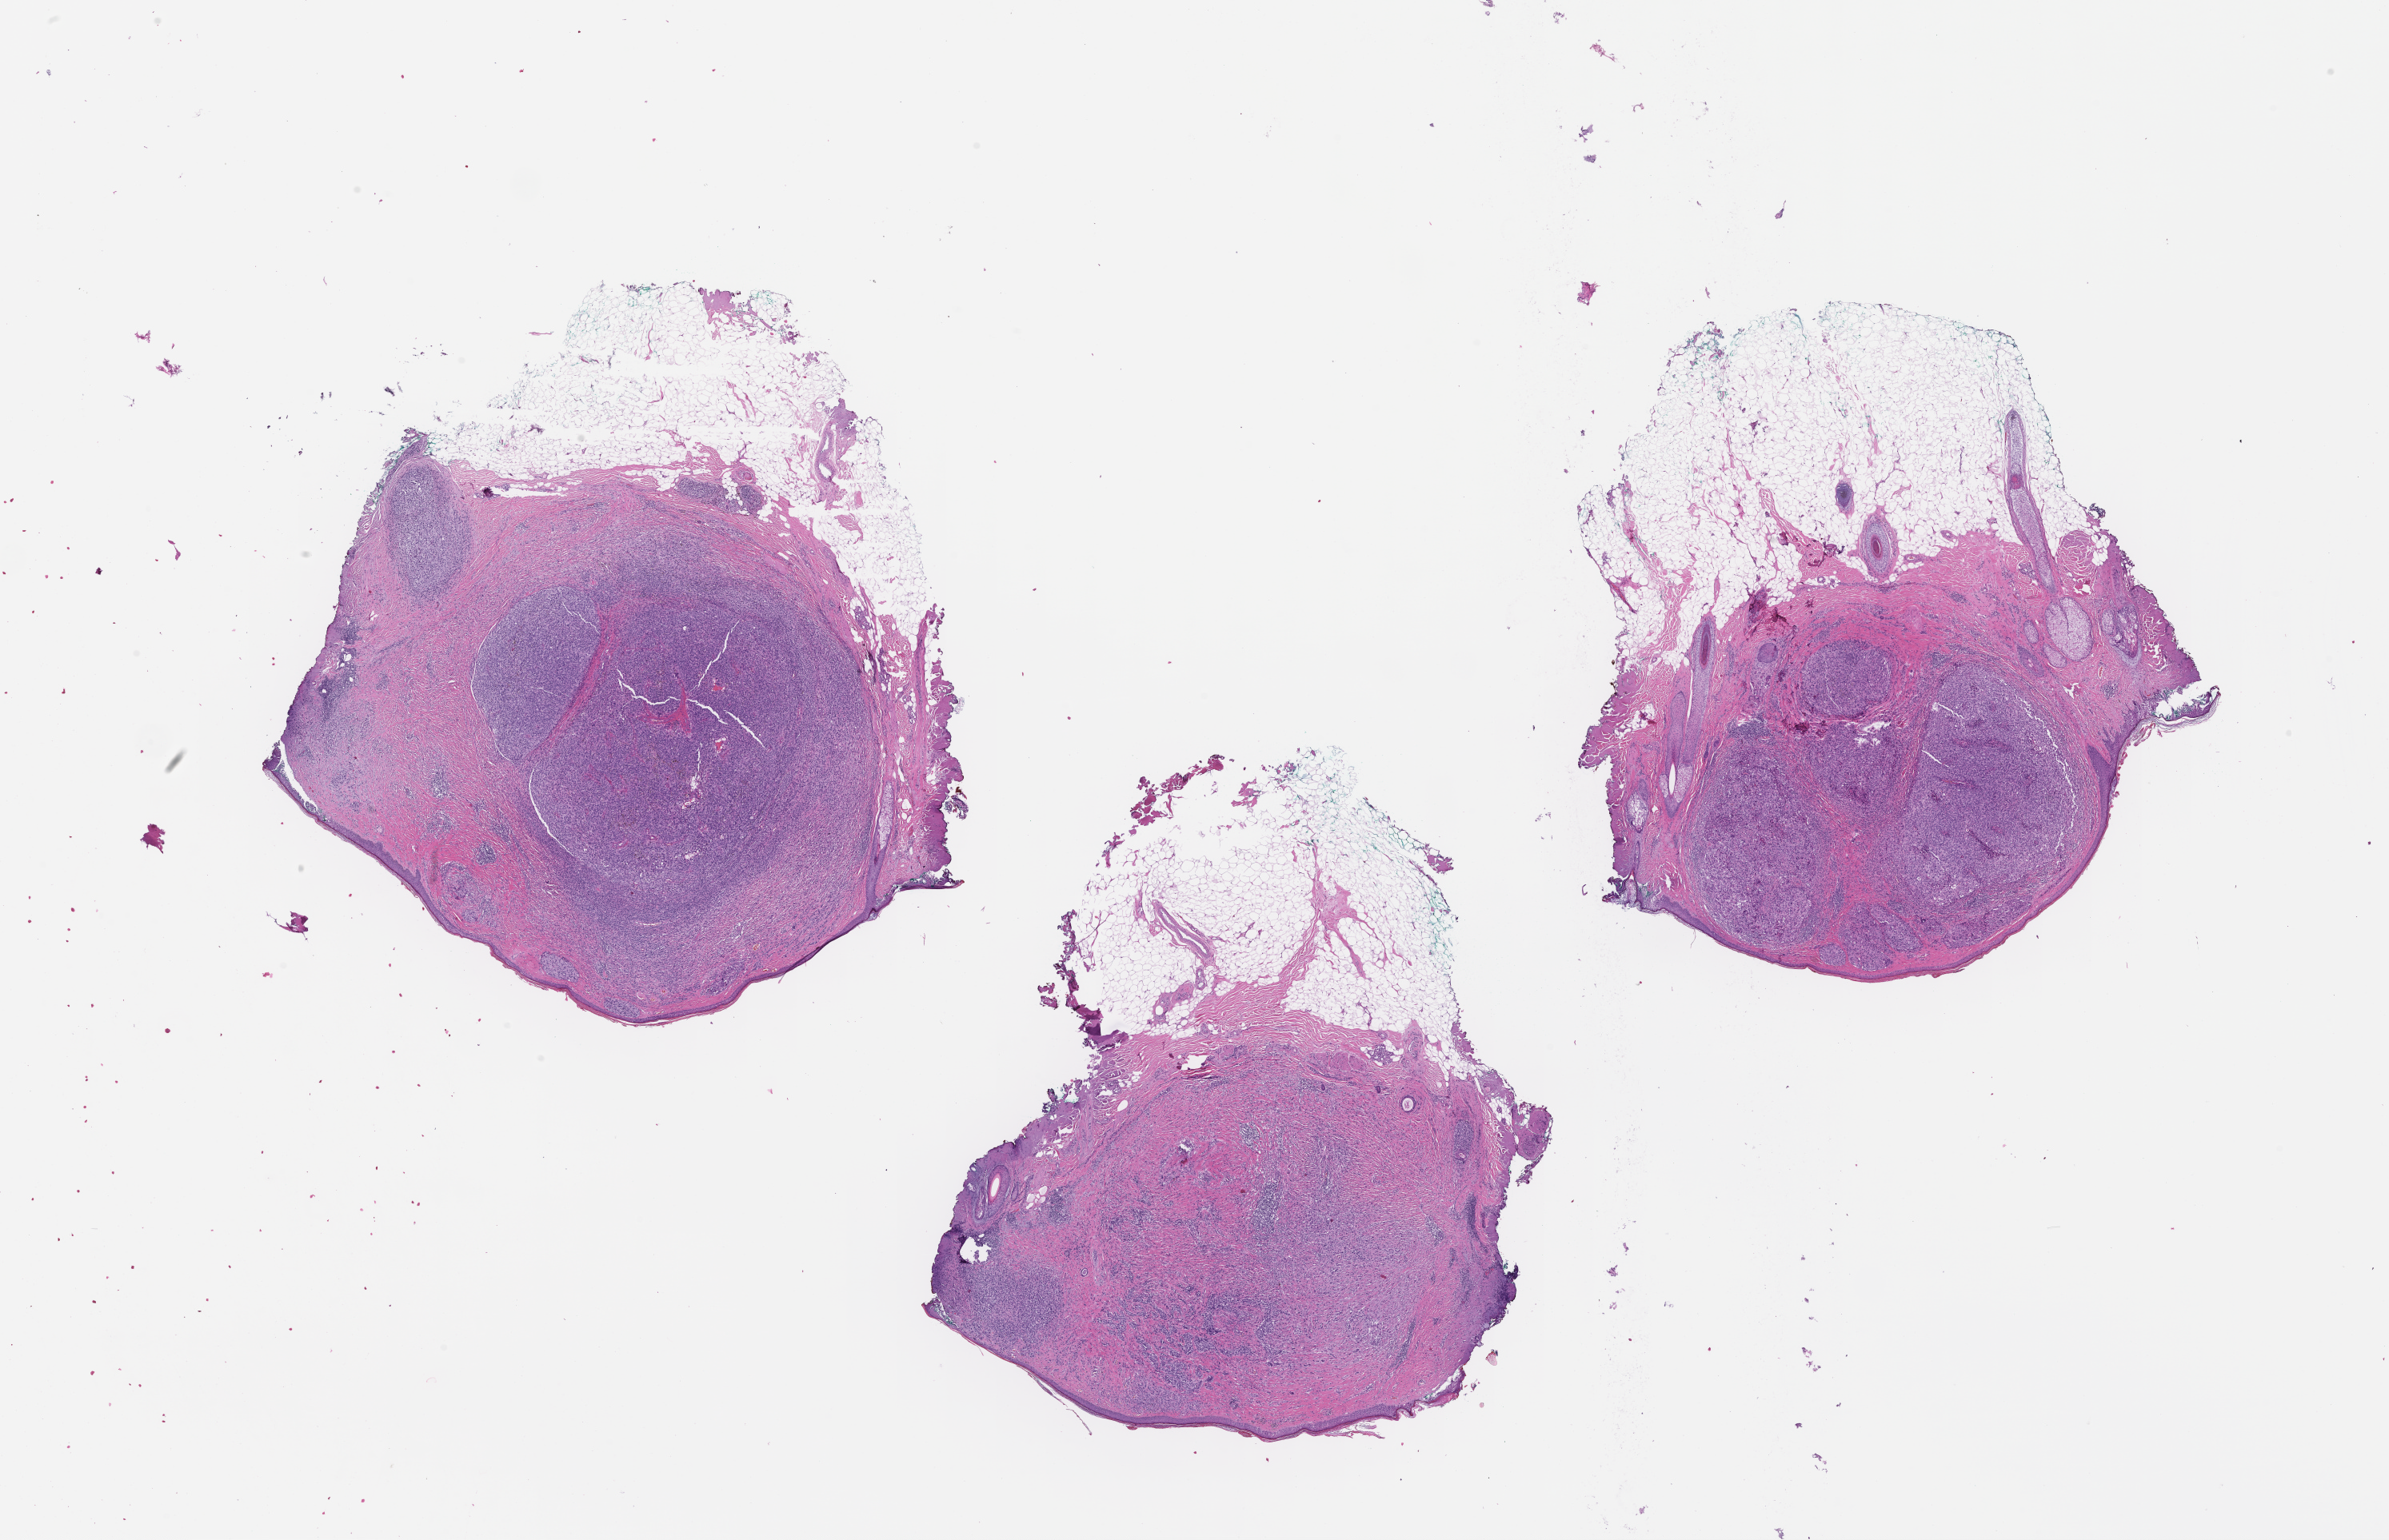
H&E whole-slide image, low-resolution overview of the scanned area, about 24.1 x 15.6 mm, formalin-fixed, paraffin-embedded (FFPE) tissue, tissue site: skin, archival tissue. Patient: male.
This section: primary tumour tissue. Diagnosis: Melanoma.